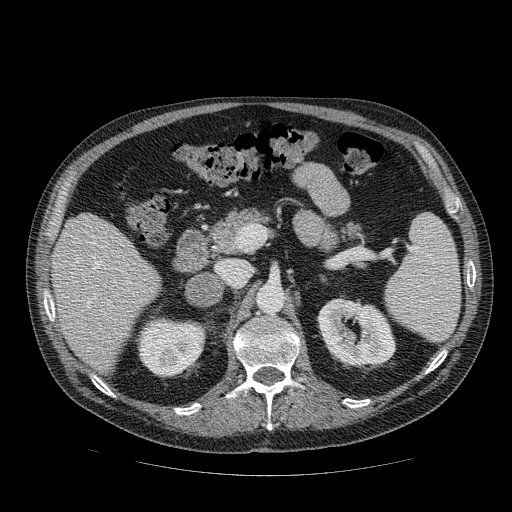
Contrast-enhanced abdominal CT, one axial slice. Position 48 of 111 along the scan axis. Reconstruction kernel STANDARD. Intravenous contrast given. Soft-tissue window (W 400 / L 40 HU). 2.5 mm slice thickness. 512 × 512 image matrix. Male patient, age 56 years. From the clinical record (not read from this slice): diagnosis: adrenocortical carcinoma; tumour side: right adrenal; tumour size at pathology: 9 cm; Ki-67 index: 48 %; stage (as recorded): 4.
Outlined on this slice (semi-automatic segmentation, software-assisted and operator-edited):
- mass: box from (x=187, y=273) to (x=222, y=306) px